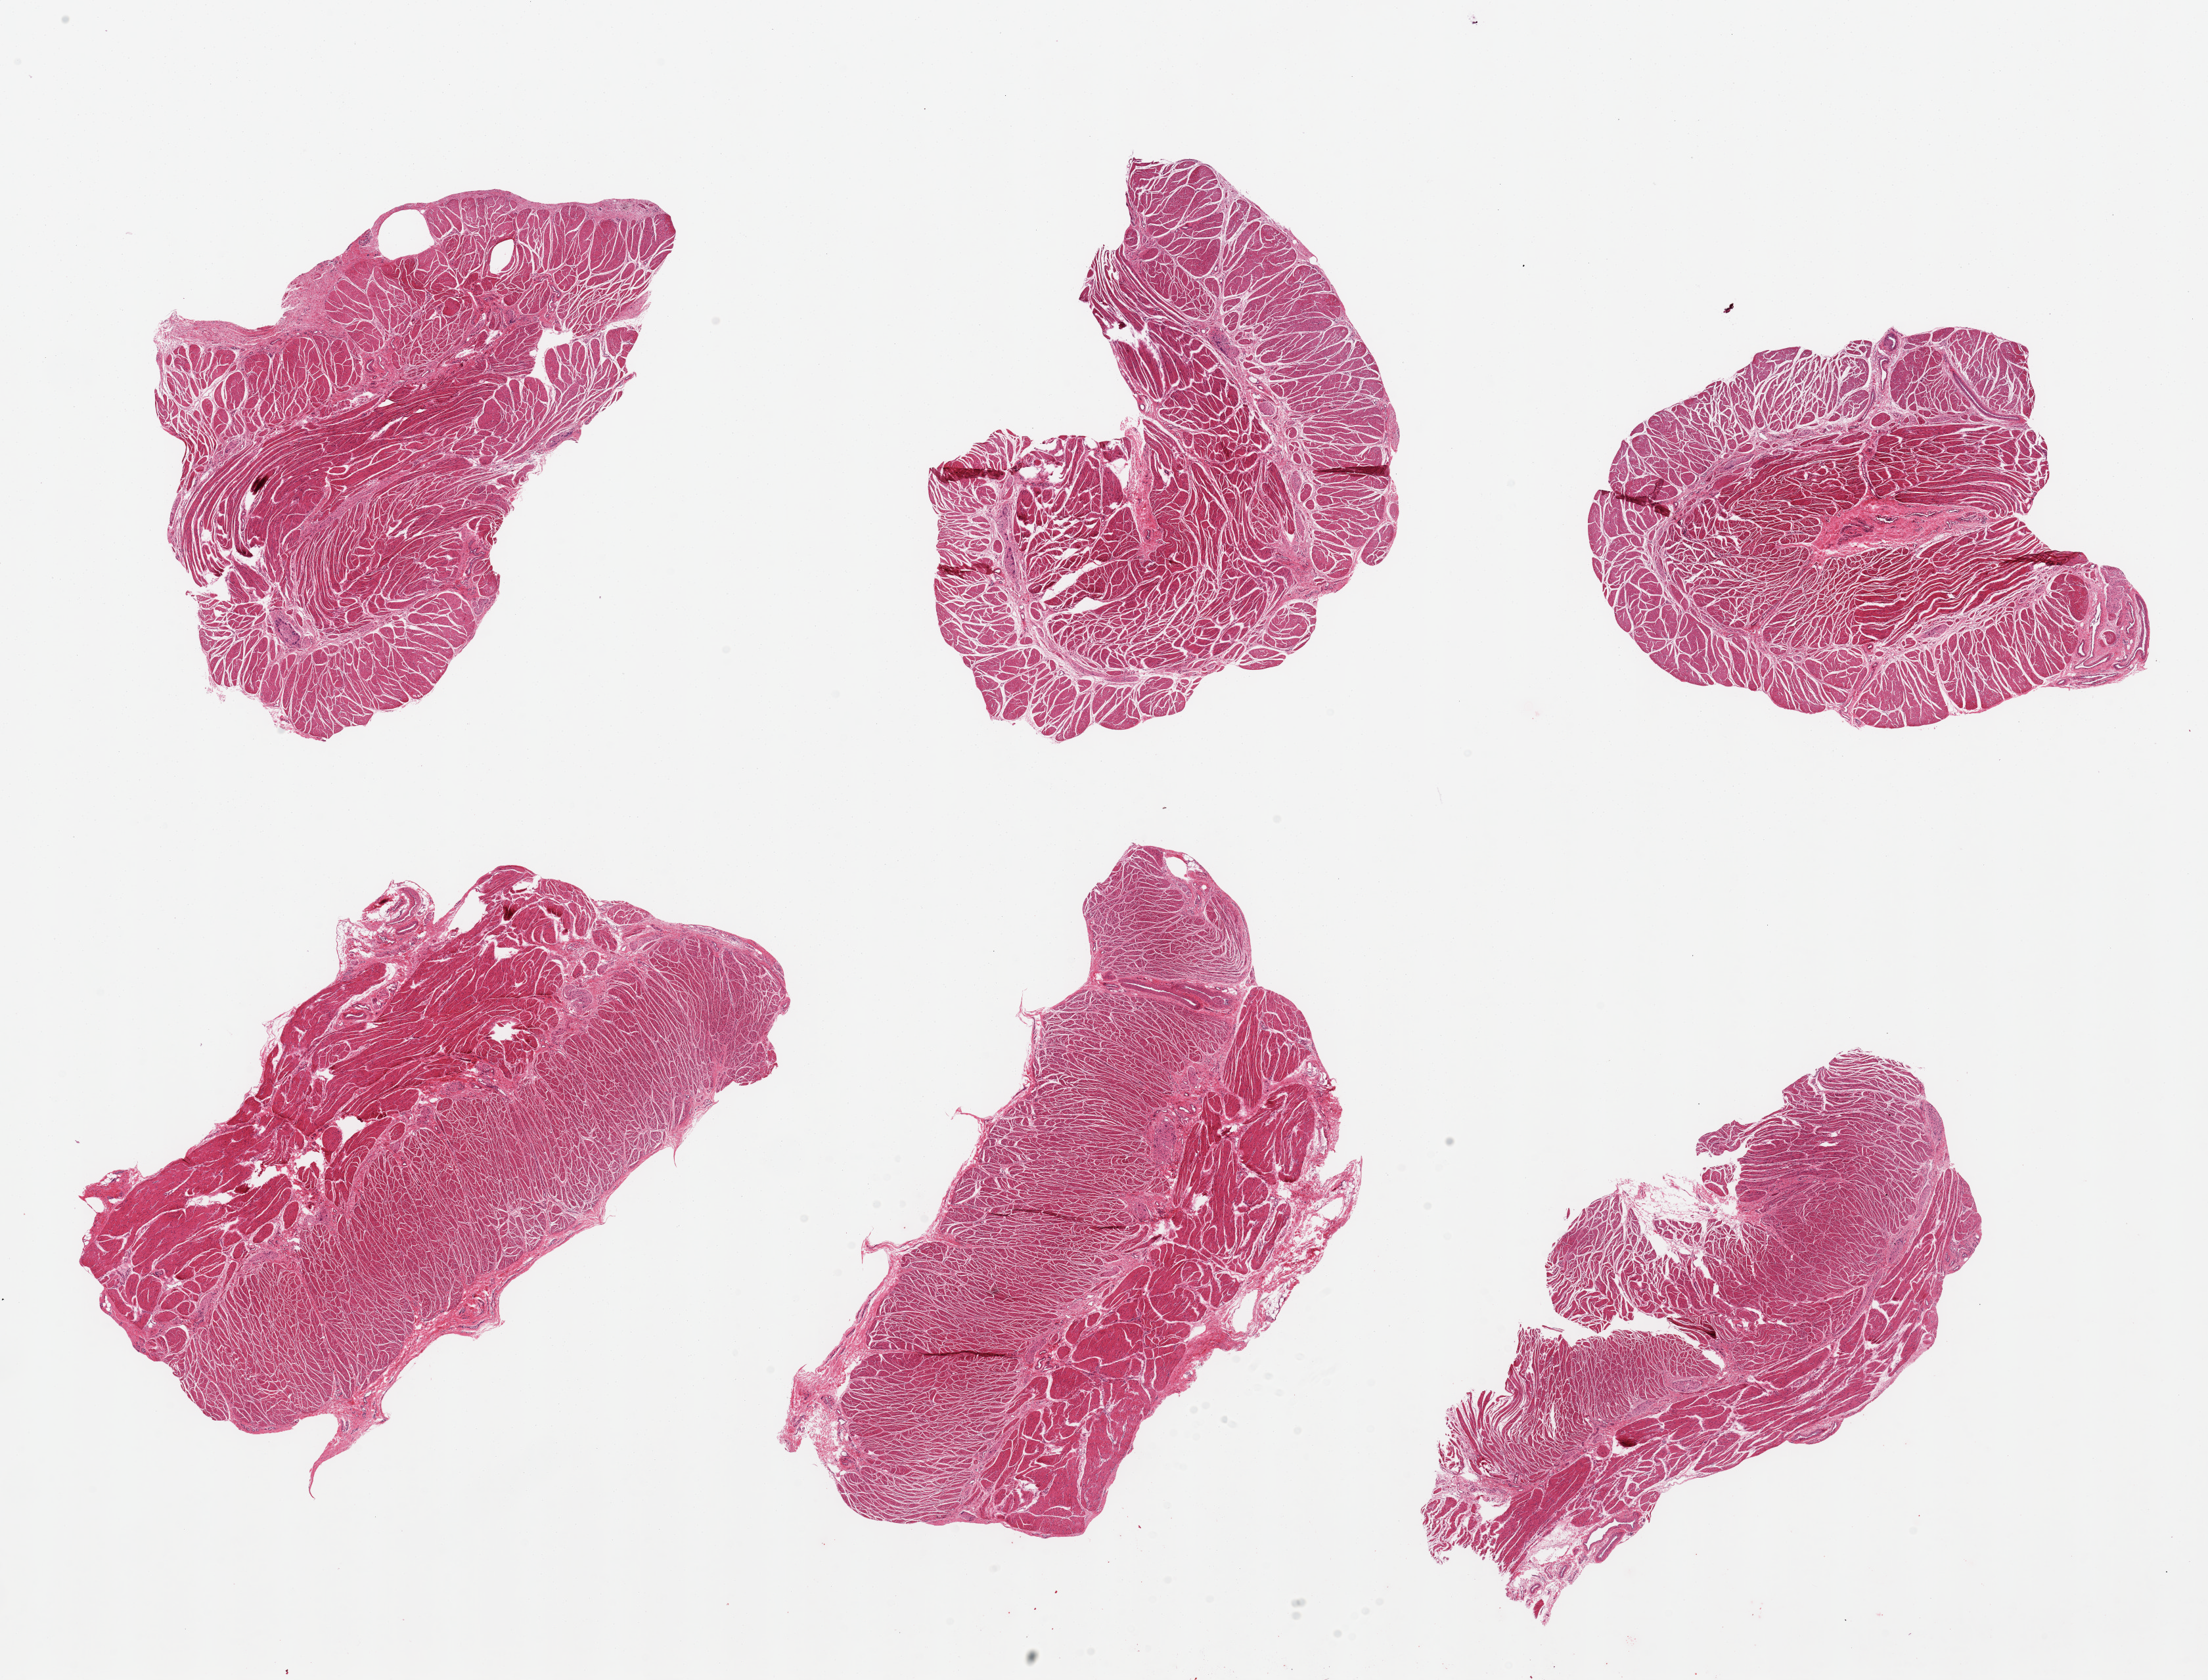
Digitized H&E-stained section, shown as a low-resolution overview of the whole scanned area (about 26.6 x 20.2 mm). PAXgene-fixed paraffin-embedded (PFPE) section. Target tissue: gastroesophageal junction. Tissue donor sample. Male donor.
Review note (as recorded): 6 pieces; well dissected muscularis.